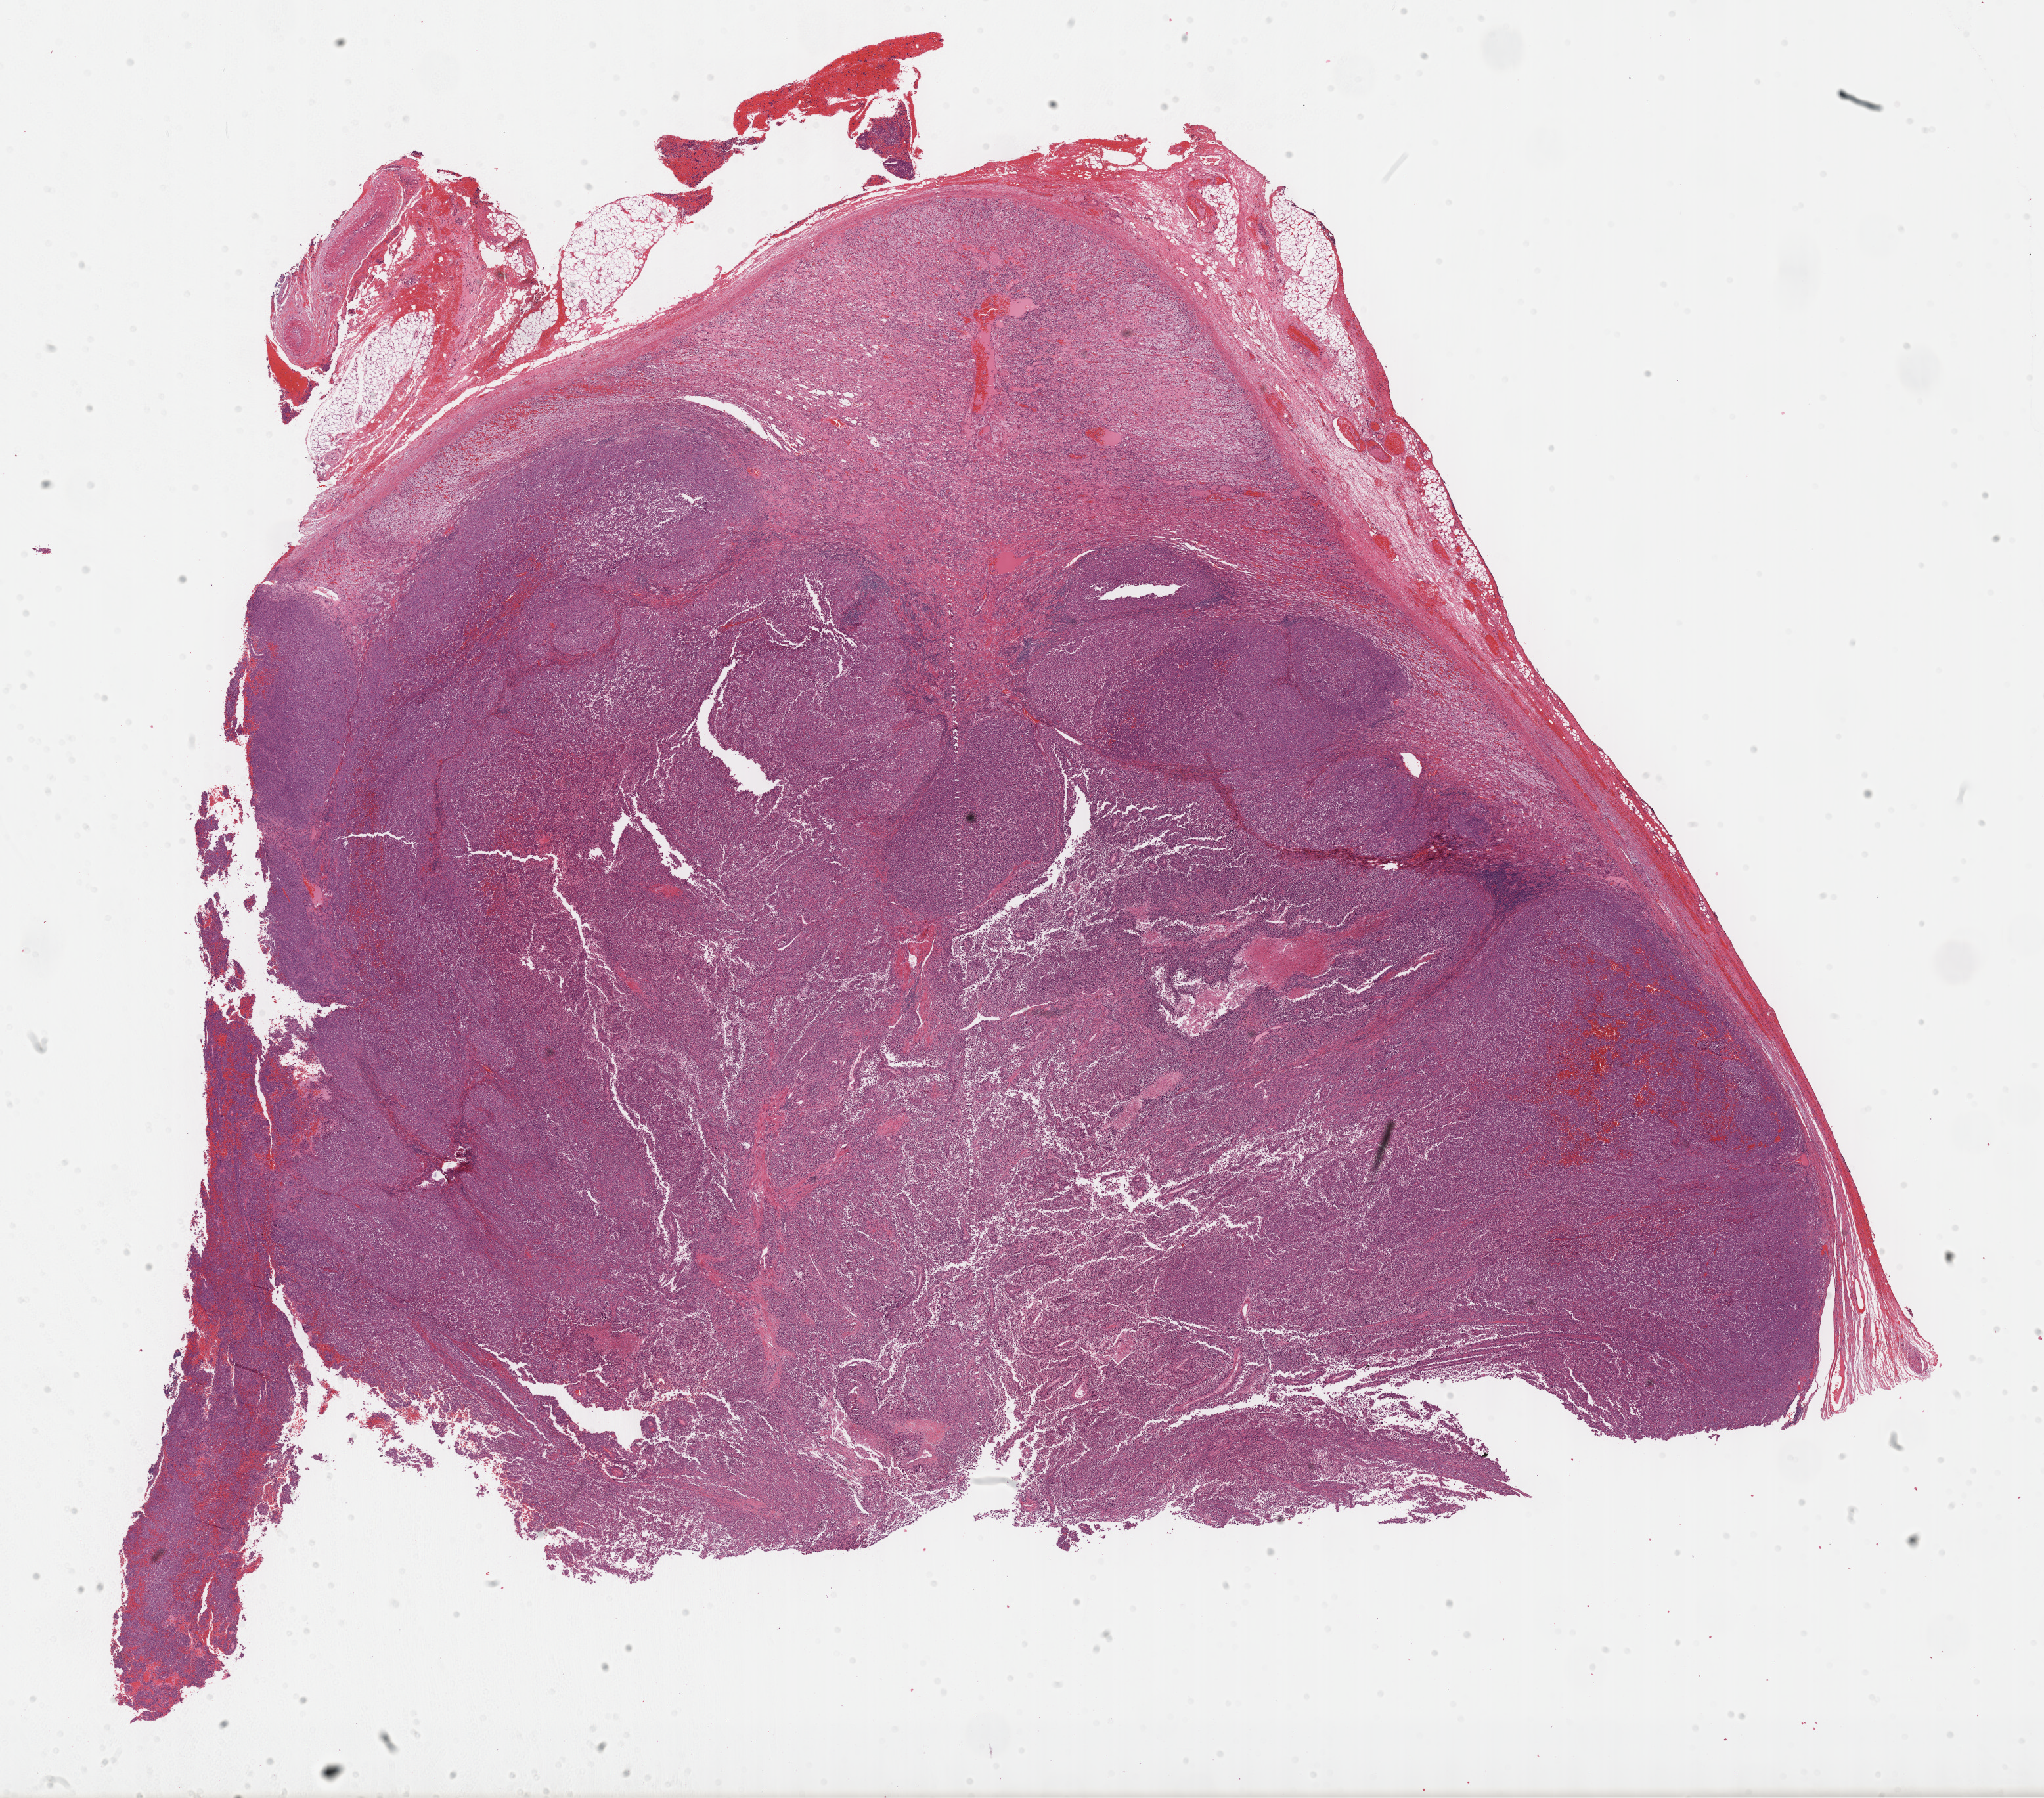
Whole-slide histology image, H&E-stained — whole scanned area (about 25.2 x 22.1 mm) shown as a low-resolution overview, FFPE section, adrenal cortex, primary tumour sample. Male patient; age at initial diagnosis 52 years.
• laterality: right
• pathologic diagnosis: Adrenal cortical carcinoma (cortex of adrenal gland)